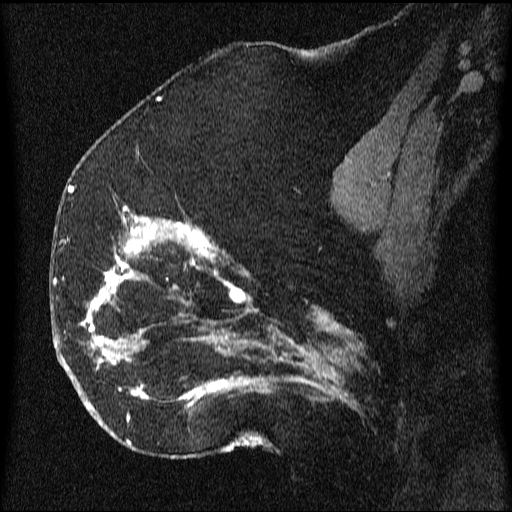
Breast MRI (dynamic contrast-enhanced), one sagittal slice; position 30 of 64 along the scan axis; dynamic contrast-enhanced series, image 2 of 3 at this slice position (ordered by acquisition); 1.5 T; TE 4.2 ms, TR 9.1 ms; 2.2 mm slice thickness; 512 × 512 image matrix. Female patient, age 52 years.
Annotated regions visible in this slice (semi-automatically segmented with operator editing):
- analysis volume of interest (the breast-tissue region the enhancement analysis was run in; not a lesion): bounding box <61,203,350,438> (left, top, right, bottom; pixels)
- tumour enhancement mask (voxels above the 70 % enhancement threshold inside the analysis volume of interest): <63,207,340,423>